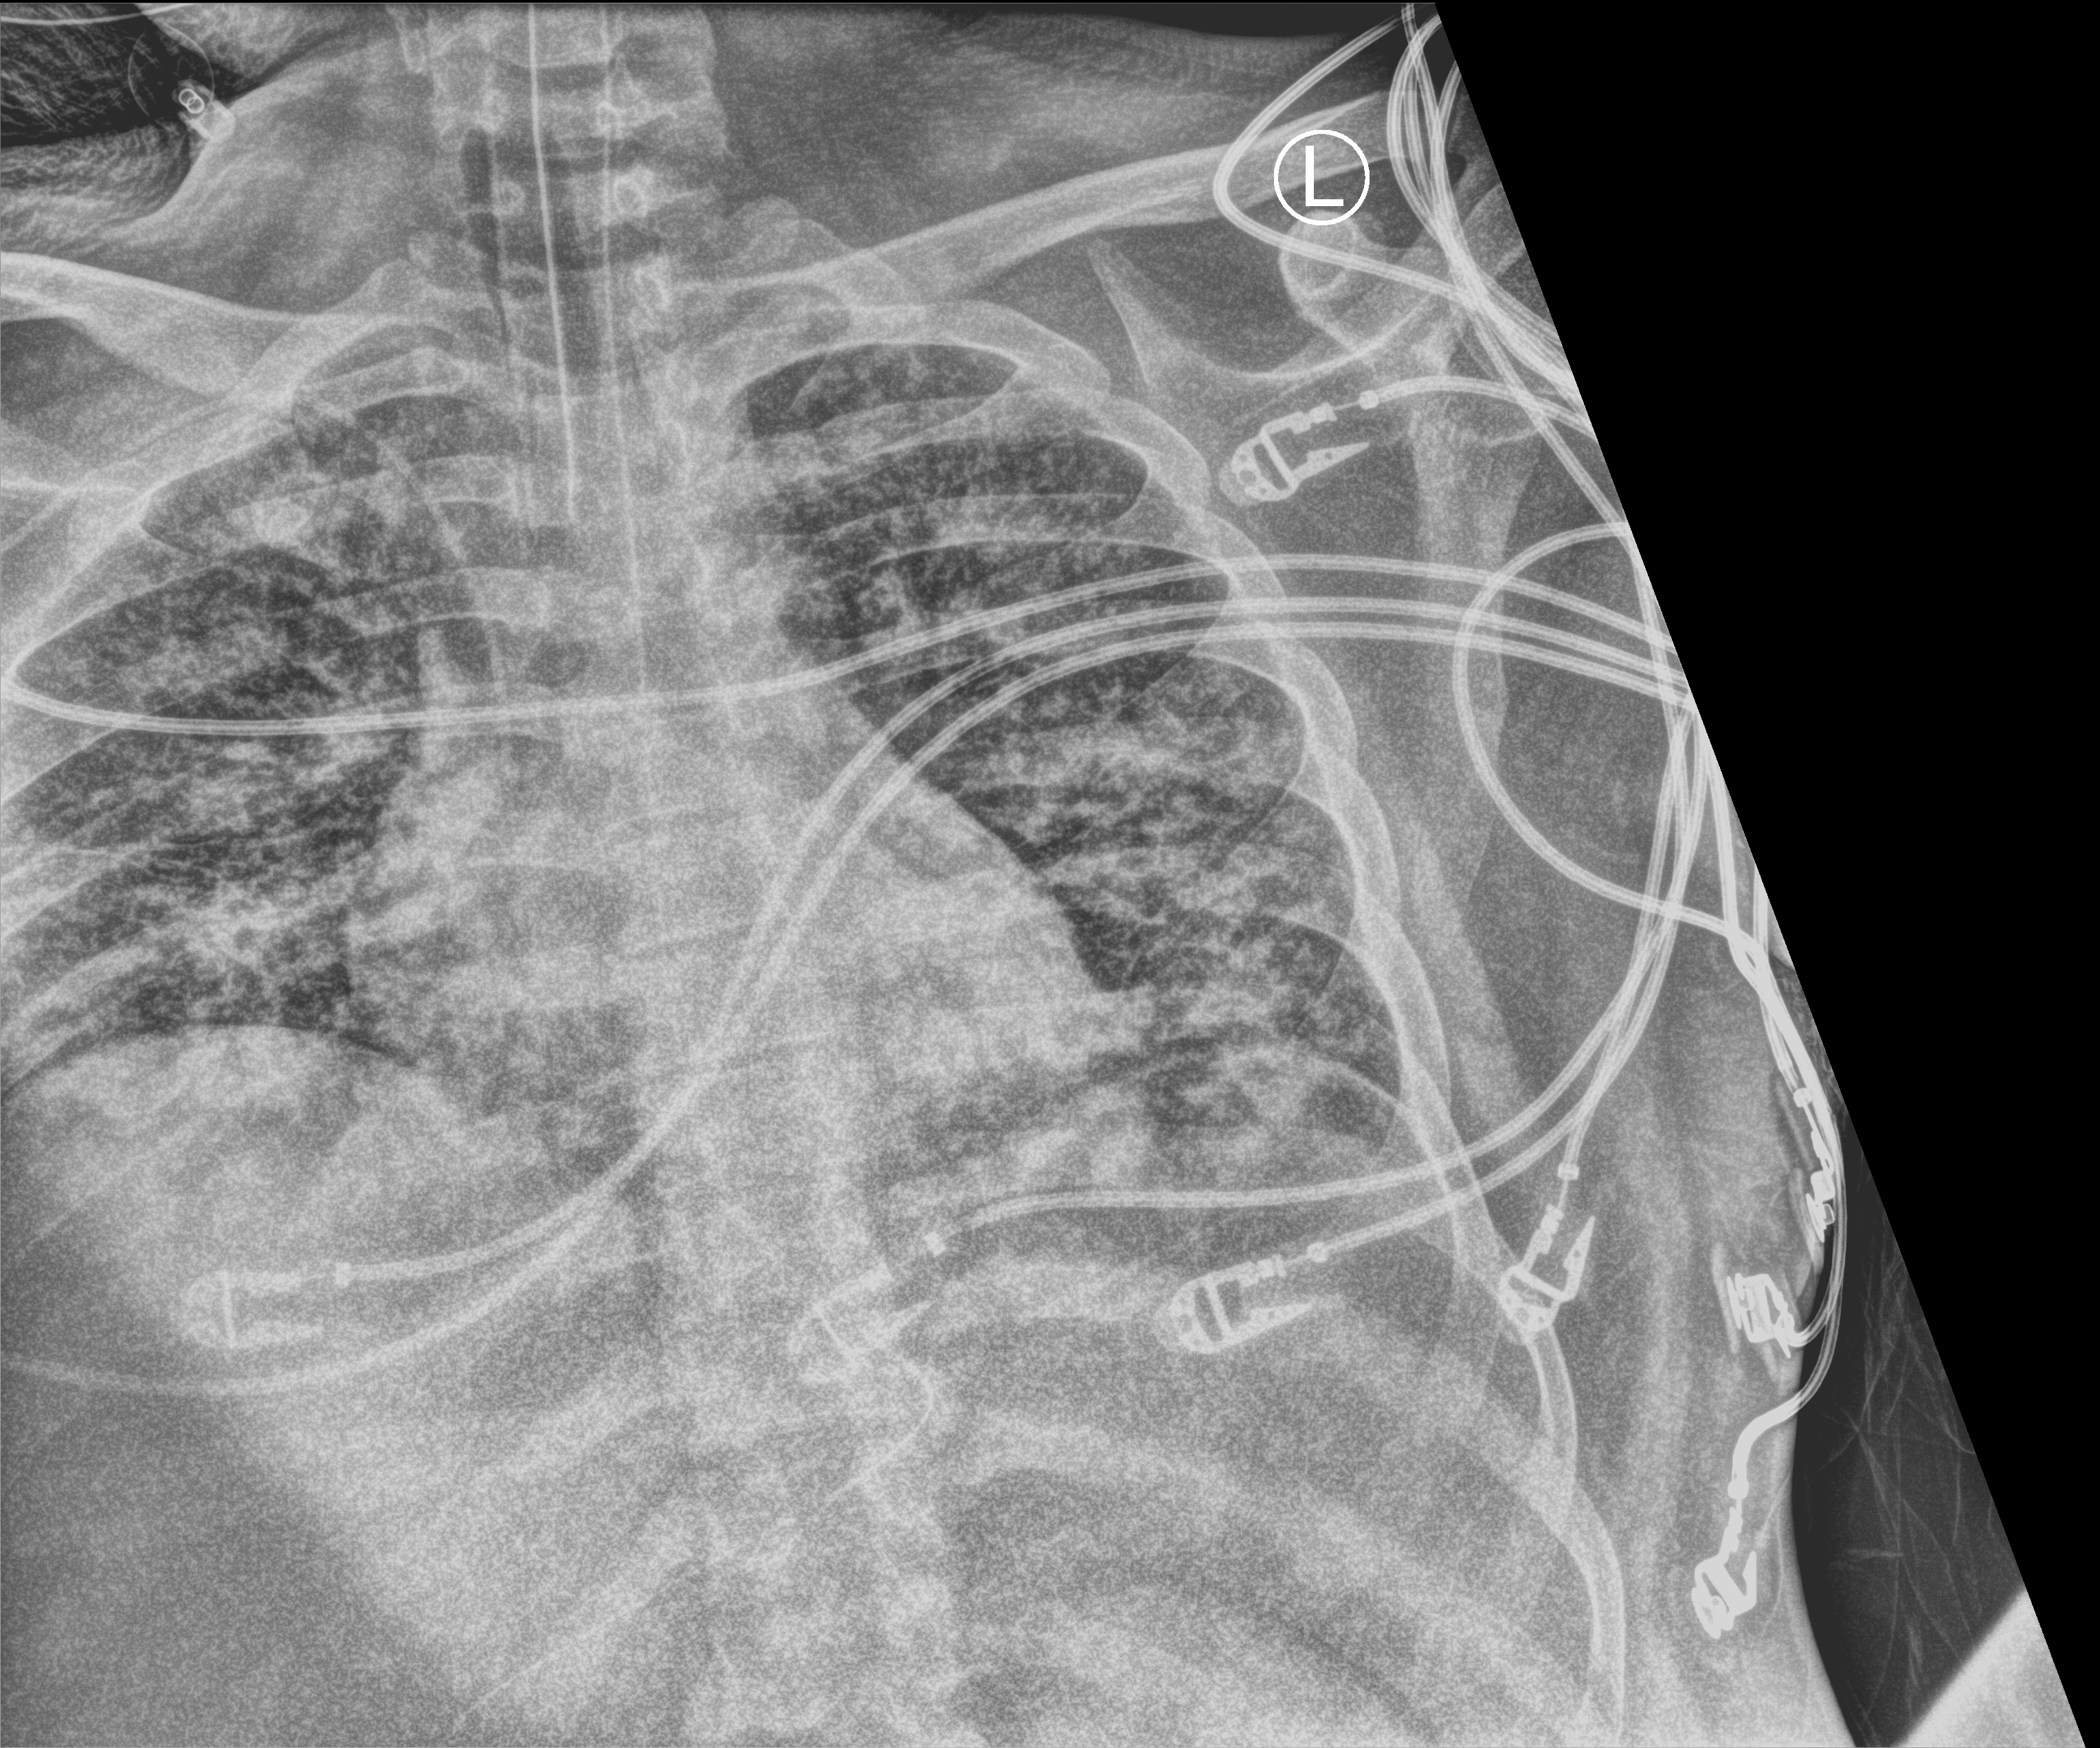
Bedside chest radiograph (computed radiography). Male patient hospitalised with COVID-19, age 18–59 years.
Hospital-stay facts (about this admission, not read from this image; timing relative to this image not recorded): length of hospital stay: 44 days; admitted to intensive care during this hospital stay: yes.